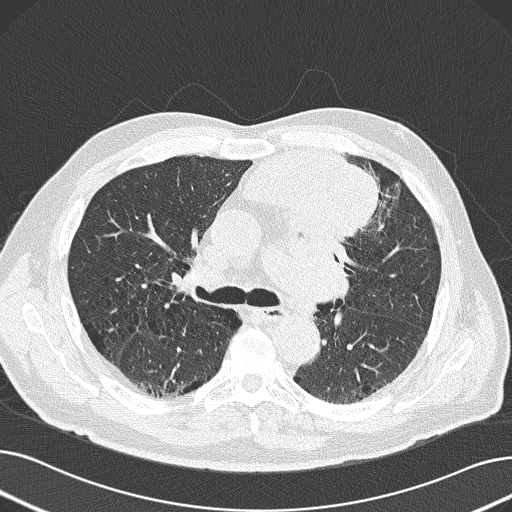
Low-dose screening chest CT, axial slice; baseline annual screen; lung window (W 1500 / L -600 HU); slice 70 of 165 in the series. Male, age 69 years at enrolment. Former smoker at enrolment.
Expert-annotated lung lesion, bounding box [x1, y1, x2, y2] px = [233, 137, 383, 251]. The exam's reader record, not a measurement of the box and not confirmed to be the same lesion: non-calcified nodule or mass ≥4 mm, left upper lobe, 6 × 10 mm, spiculated (stellate) margins, soft tissue attenuation. Later outcome: lung cancer diagnosed 20 days after this screen — non-small cell carcinoma, left upper lobe, poorly differentiated (G3), stage IB (AJCC 6th edition), 100 mm at pathology.